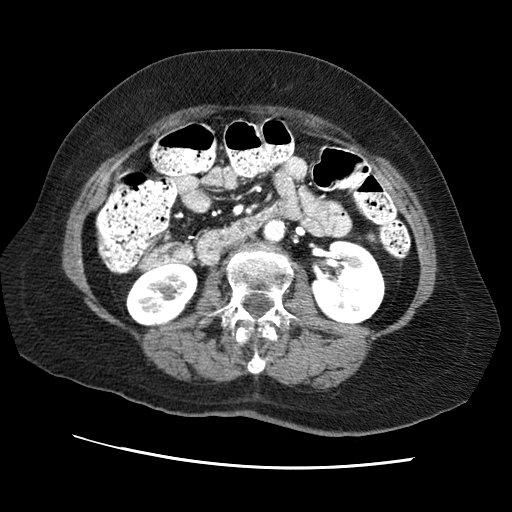
Contrast-enhanced abdominal CT (liver protocol), one axial slice; slice 9 of 65 in the series (ordered by position); reconstruction kernel STANDARD; 120 kVp; soft-tissue window (W 400 / L 40 HU); 512 × 512 image matrix, field of view 340 × 340 mm. Case-level facts recorded for this patient, not image findings: diagnosis: hepatocellular carcinoma (patient treated with transarterial chemoembolisation; whether this scan precedes or follows treatment is not stated here); TNM stage (as recorded): Stage-II; Child-Pugh class: A; tumour differentiation: no biopsy; tumour nodularity: multinodular.
Outlined on this slice (semi-automatic segmentation, software-assisted and operator-edited):
- liver parenchyma outside the tumour (the mass and vessels are separate outlines, so this box may not span the whole liver): bounding box (x1, y1, x2, y2) in pixels: (100, 244, 104, 247)